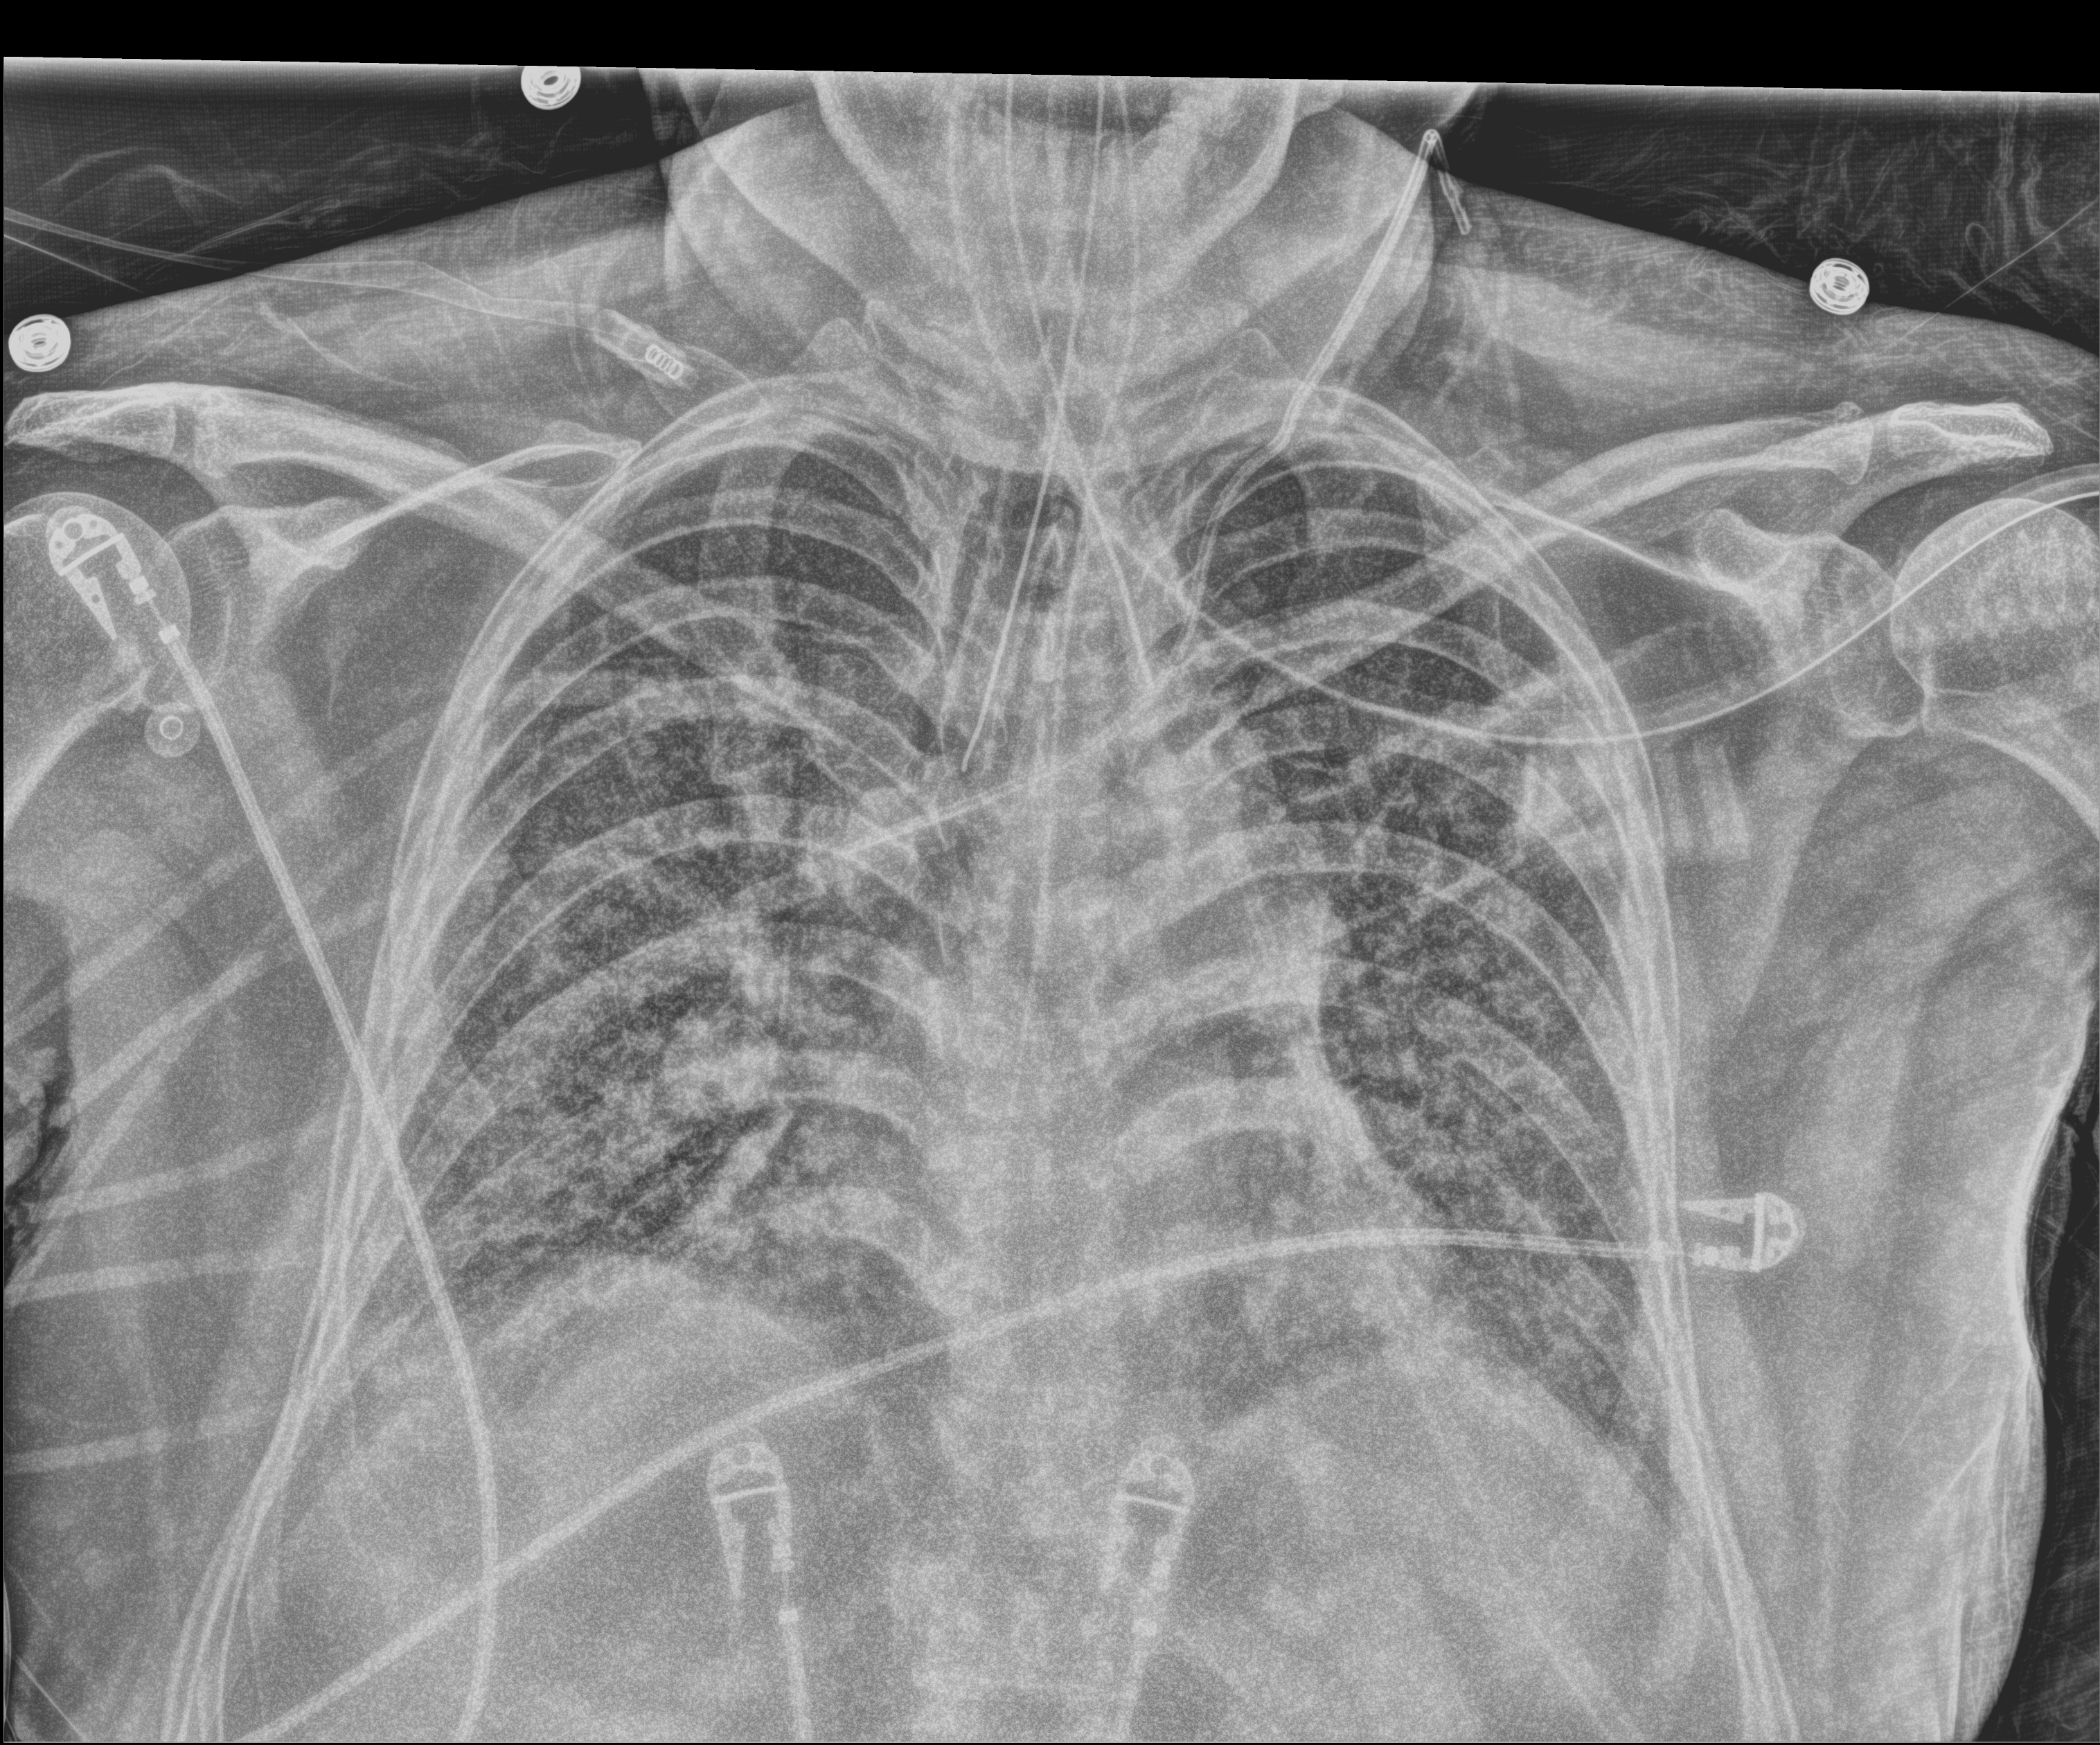
Portable chest radiograph, anteroposterior (AP) projection. Patient hospitalised with COVID-19, aged 18–59 years.
Hospital-stay facts (about this admission, not read from this image; timing relative to this image not recorded):
- admitted to intensive care during this hospital stay: yes